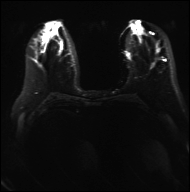
Breast MRI, one axial slice; slice 12 of 40 in the series (ordered by position); diffusion-weighted series; image 2 of 4 stored at this slice position (different b-values; order by instance number); 3 T; 190 × 192 image matrix, field of view 317 × 320 mm. Female patient.
Outlined on this slice (outlined manually by an expert reader):
- tumour on diffusion-weighted imaging: bounding box [x1, y1, x2, y2] px = [52, 47, 65, 53]